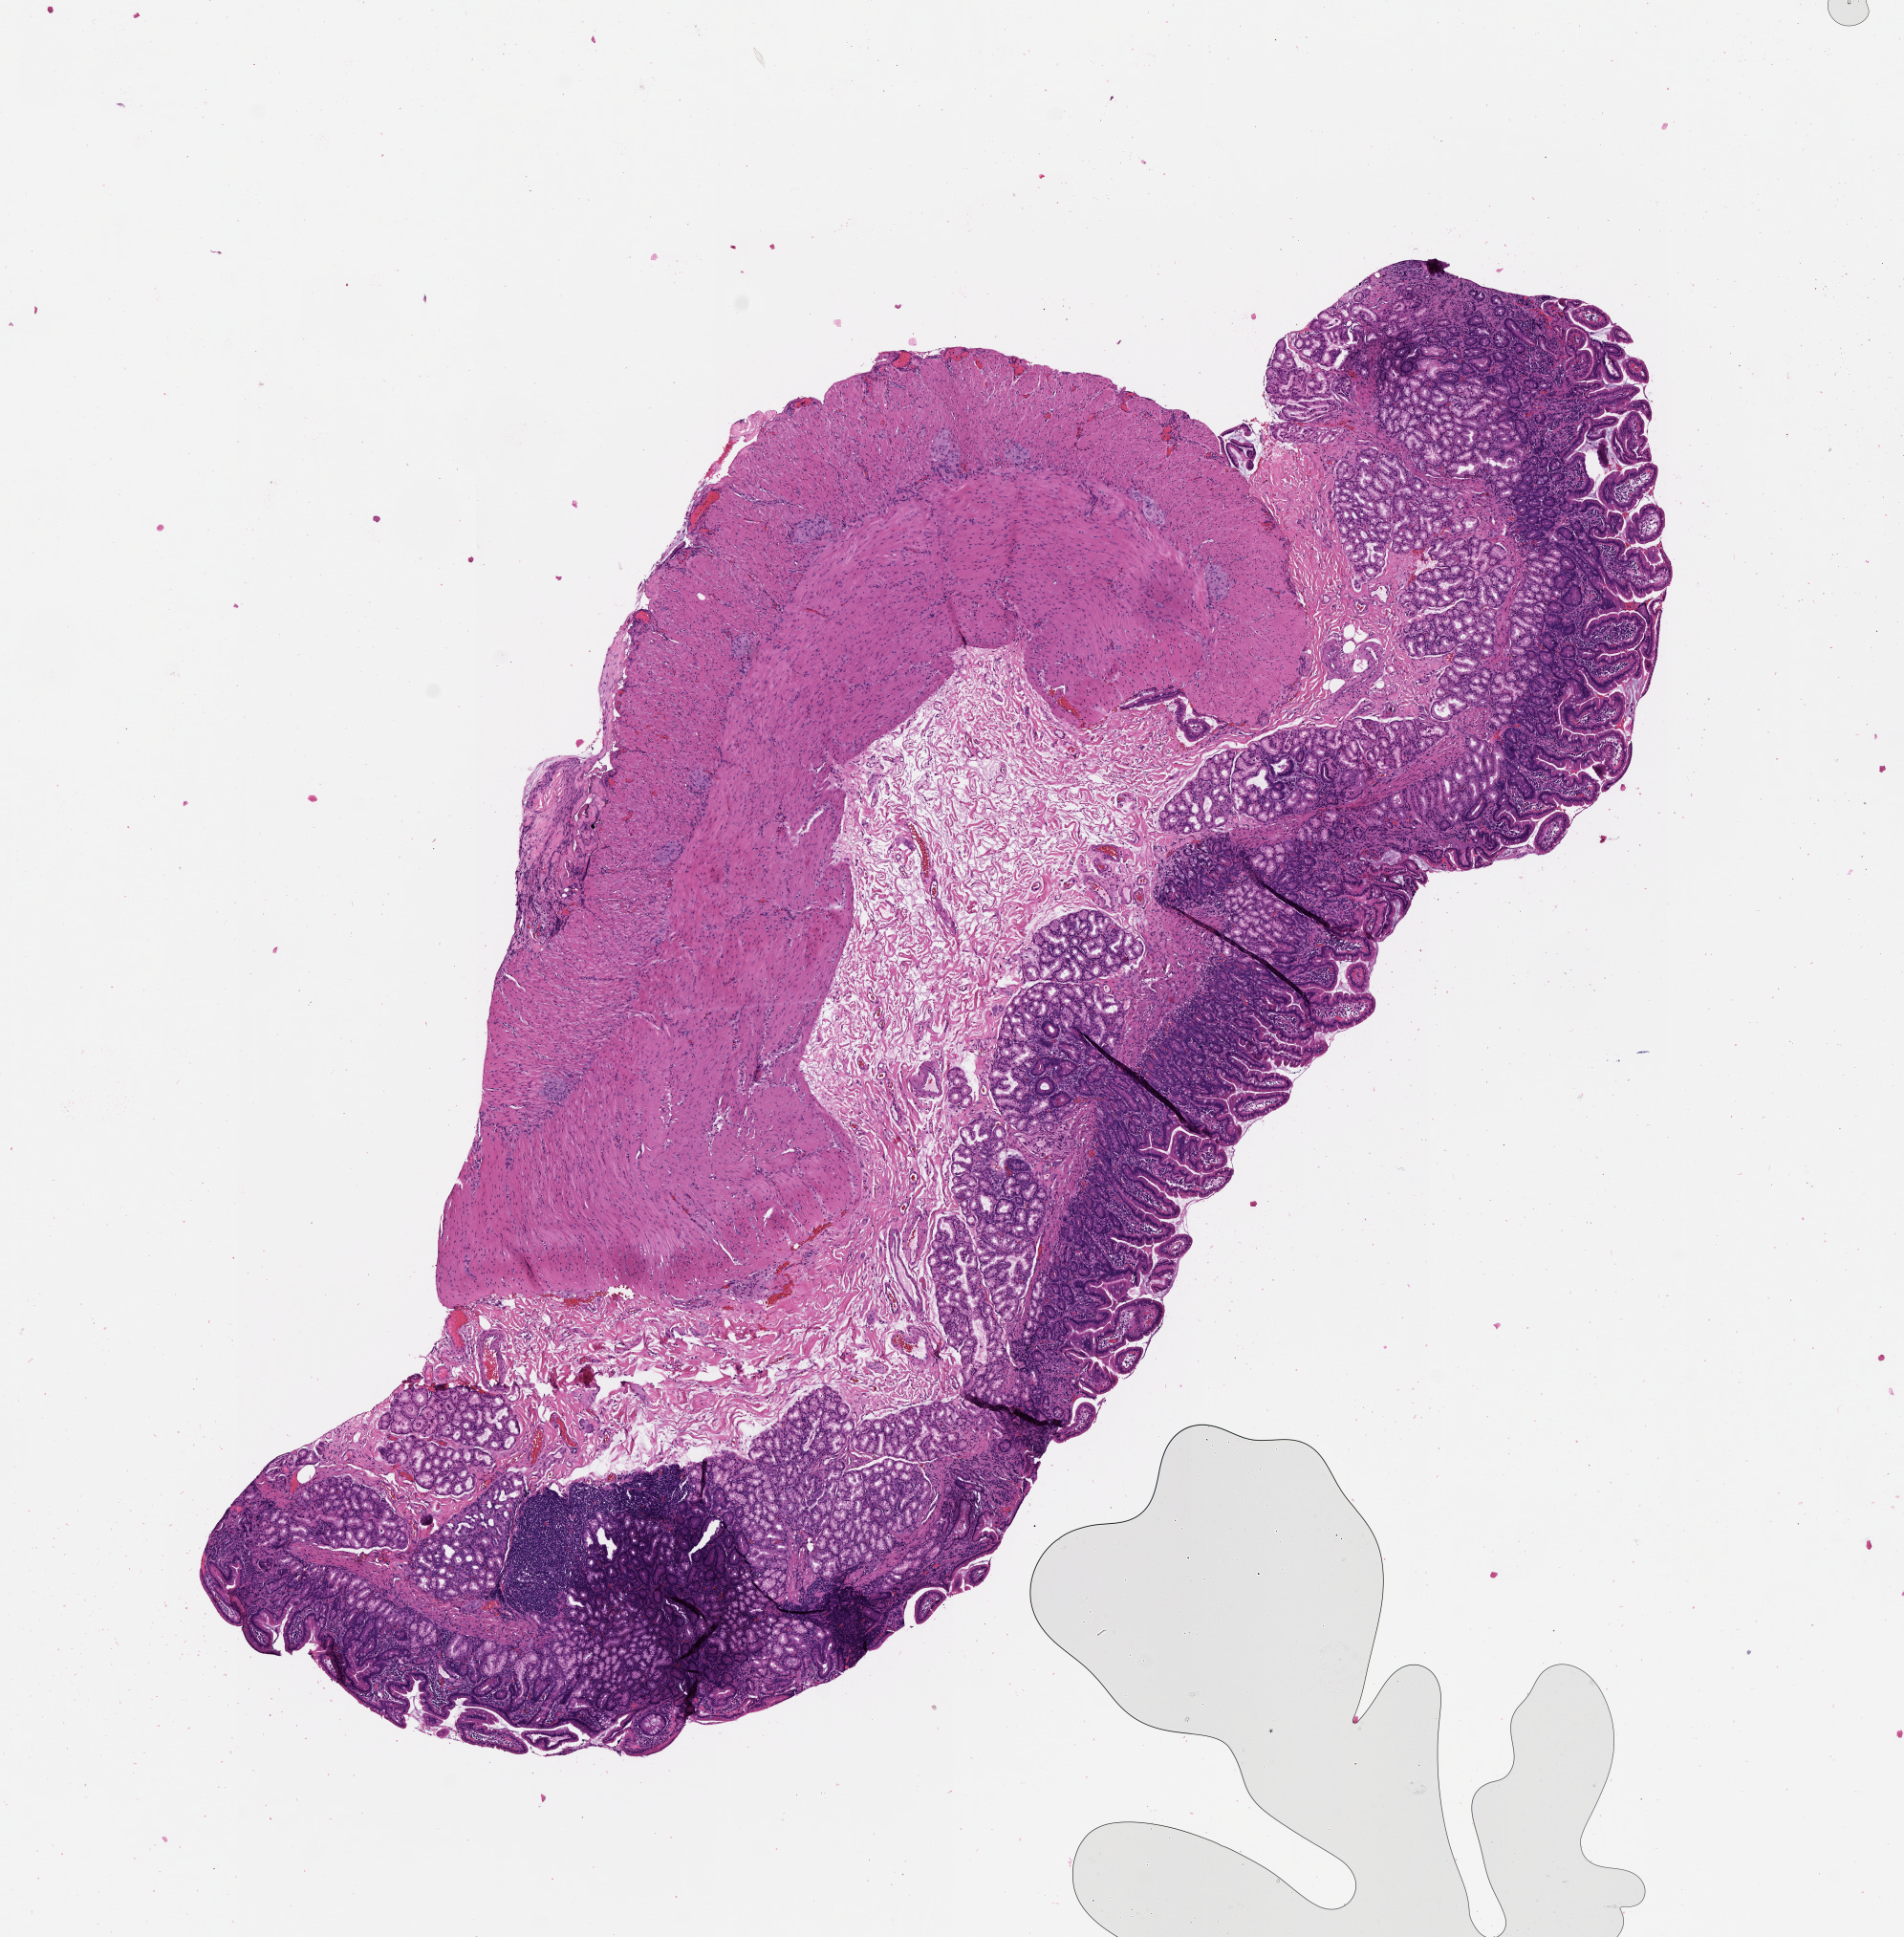
Whole-slide histology image, H&E-stained — a low-resolution overview of the entire scanned area, about 8.0 x 8.2 mm, pancreas, normal (non-tumour) tissue. 71-year-old female patient.
This section: normal (non-tumour) tissue from the same patient. Patient diagnosis: Infiltrating duct carcinoma, NOS.